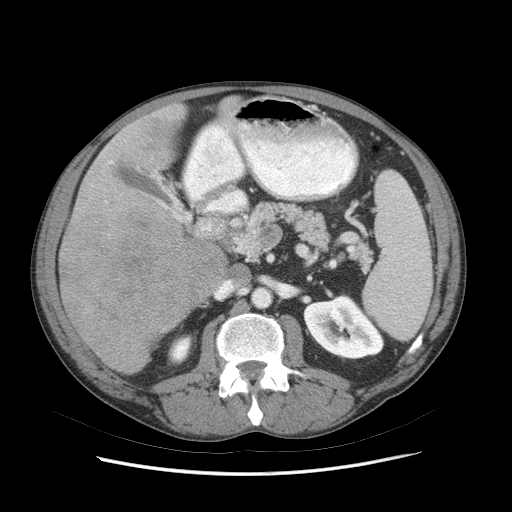
Contrast-enhanced abdominal CT (liver protocol), one axial slice; position 32 of 89 along the scan axis; 140 kVp; soft-tissue window (W 400 / L 40 HU); 512 × 512 image matrix, field of view 380 × 380 mm. Case-level facts recorded for this patient, not image findings: diagnosis: hepatocellular carcinoma (patient treated with transarterial chemoembolisation; whether this scan precedes or follows treatment is not stated here); TNM stage (as recorded): Stage-IIIB; Child-Pugh class: A; tumour nodularity: multinodular.
Structures marked on this image (semi-automatic segmentation, software-assisted and operator-edited):
- liver parenchyma outside the tumour (the mass and vessels are separate outlines, so this box may not span the whole liver): box from (x=58, y=96) to (x=238, y=374) px
- mass: (x=61, y=207)–(x=230, y=373)
- liver vessels: (x=108, y=161)–(x=113, y=164)